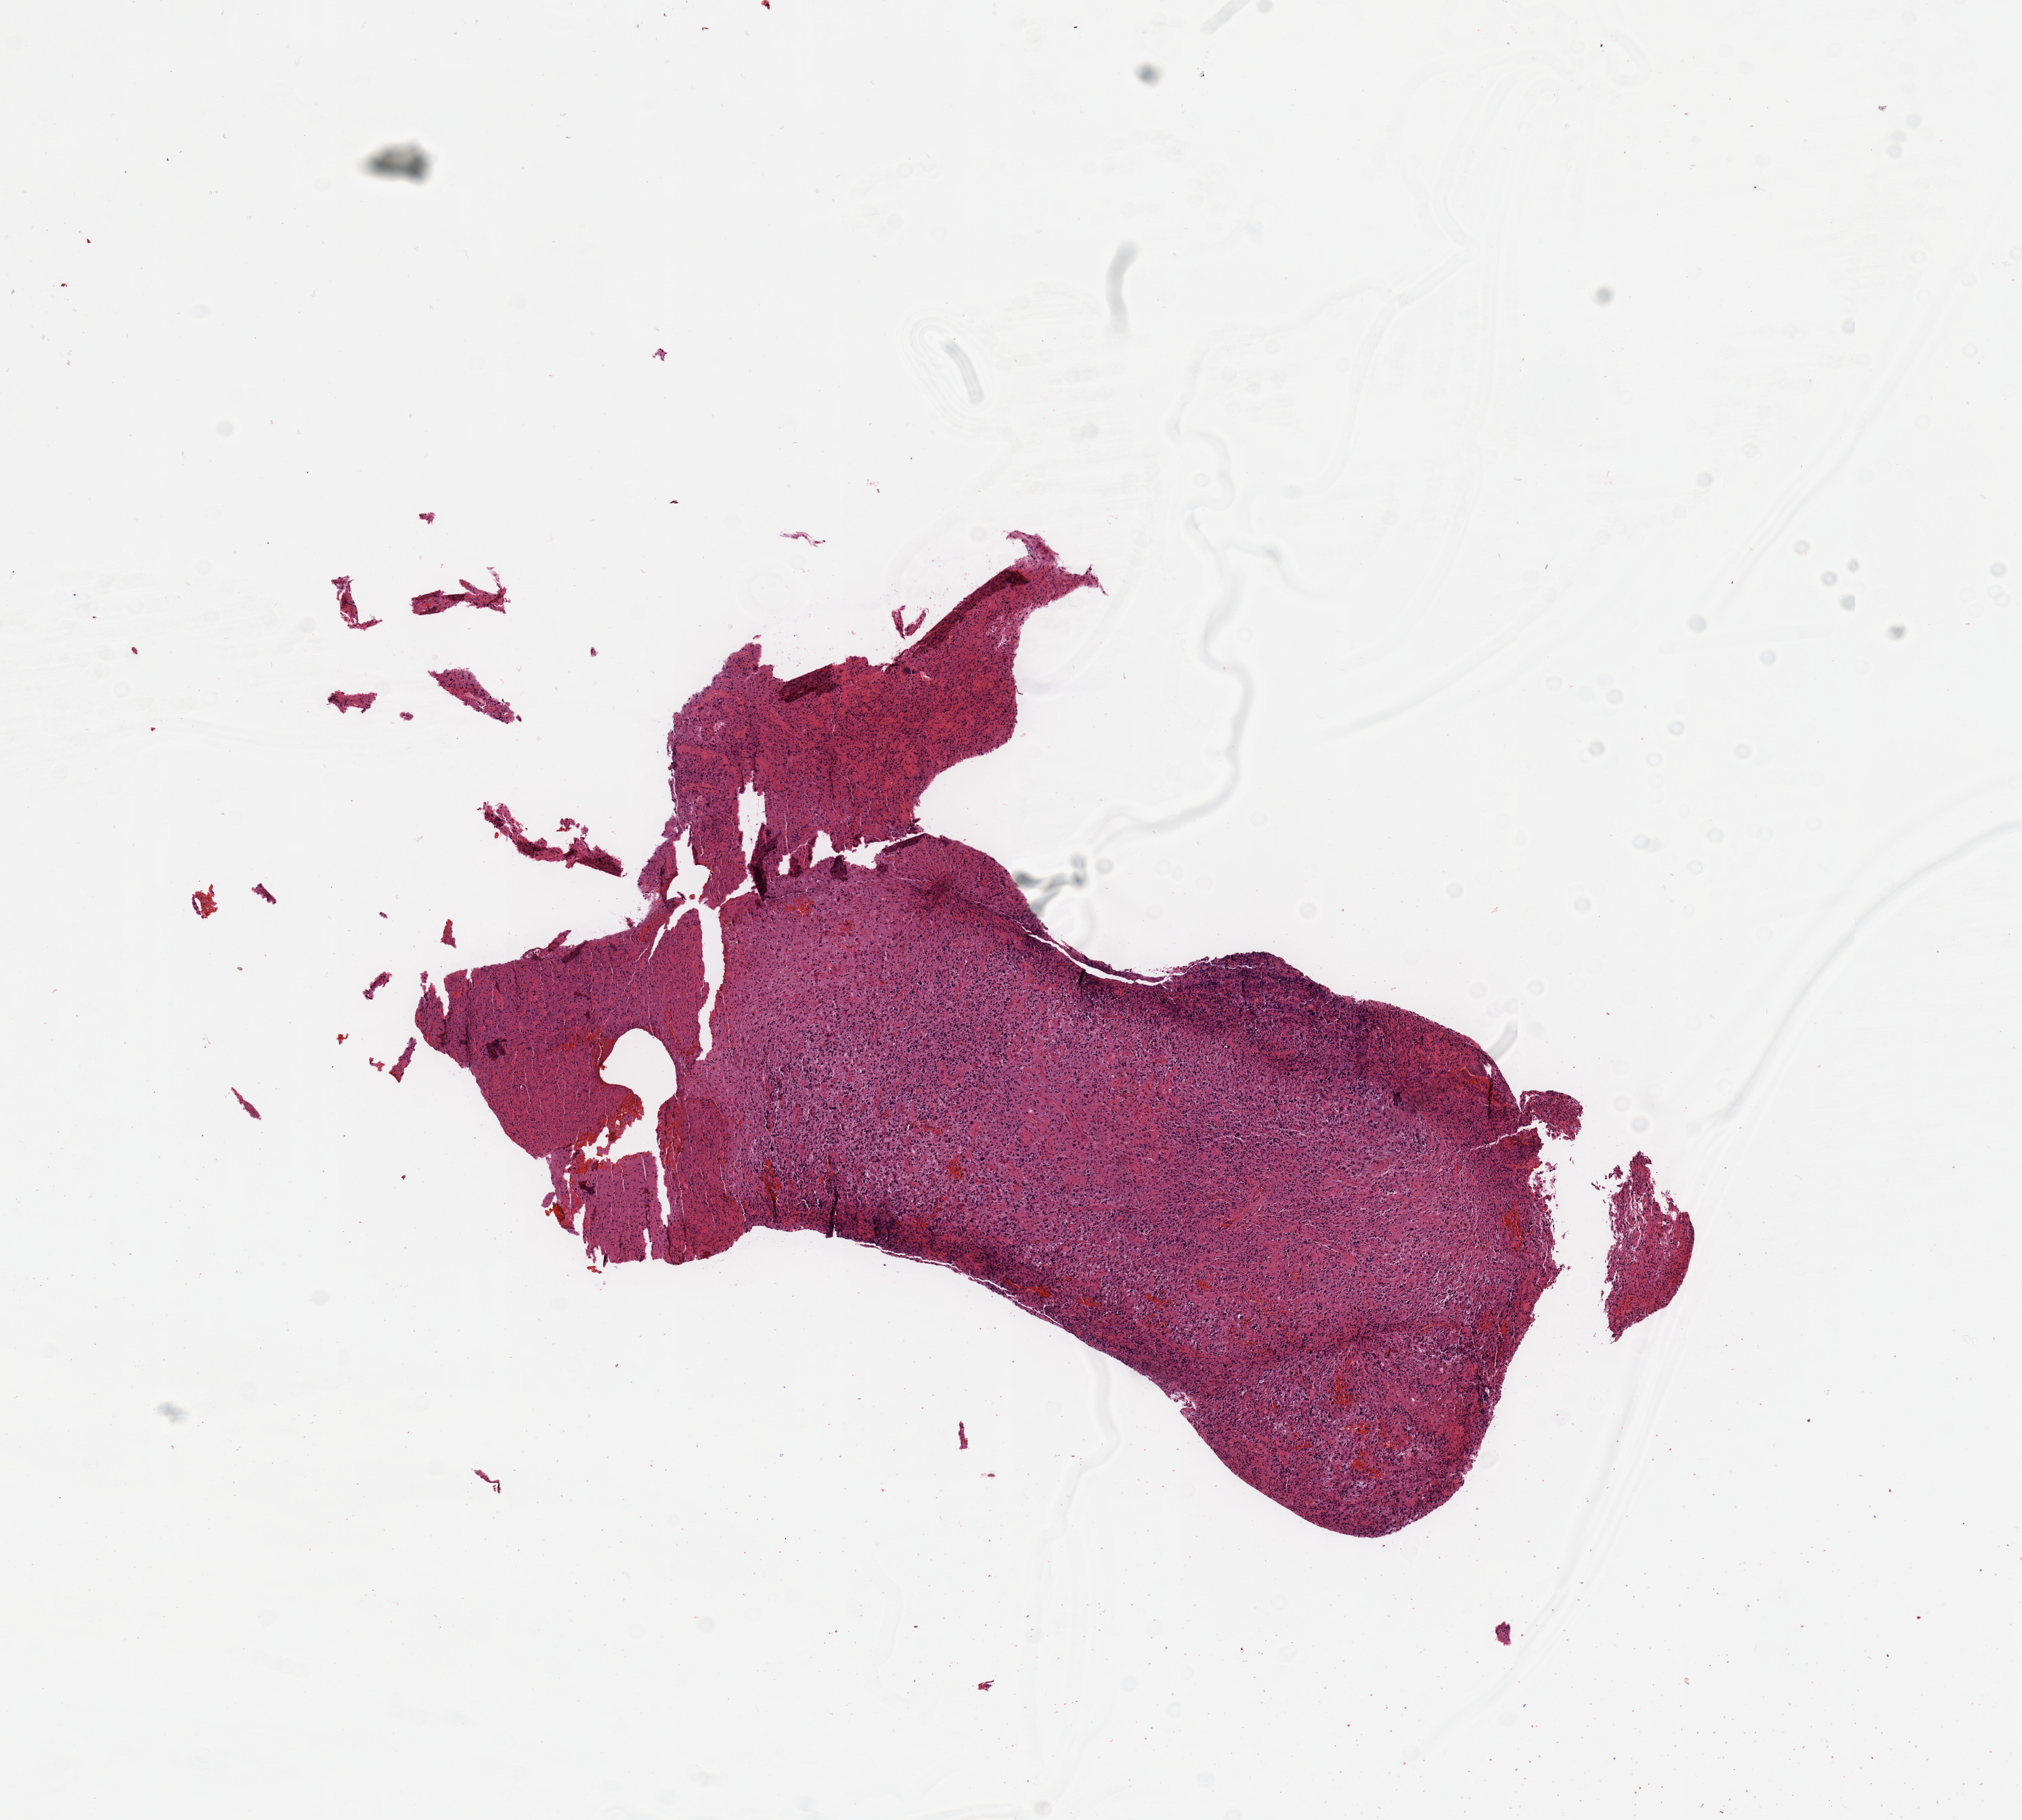
Whole-slide histology image, H&E-stained, a low-resolution overview of the entire scanned area, about 11.8 x 10.6 mm (acquisition: 20x scan), brain, tumour tissue. 51-year-old female patient.
* primary tumour site (as recorded): temporal lobe
* histologic diagnosis: Glioblastoma